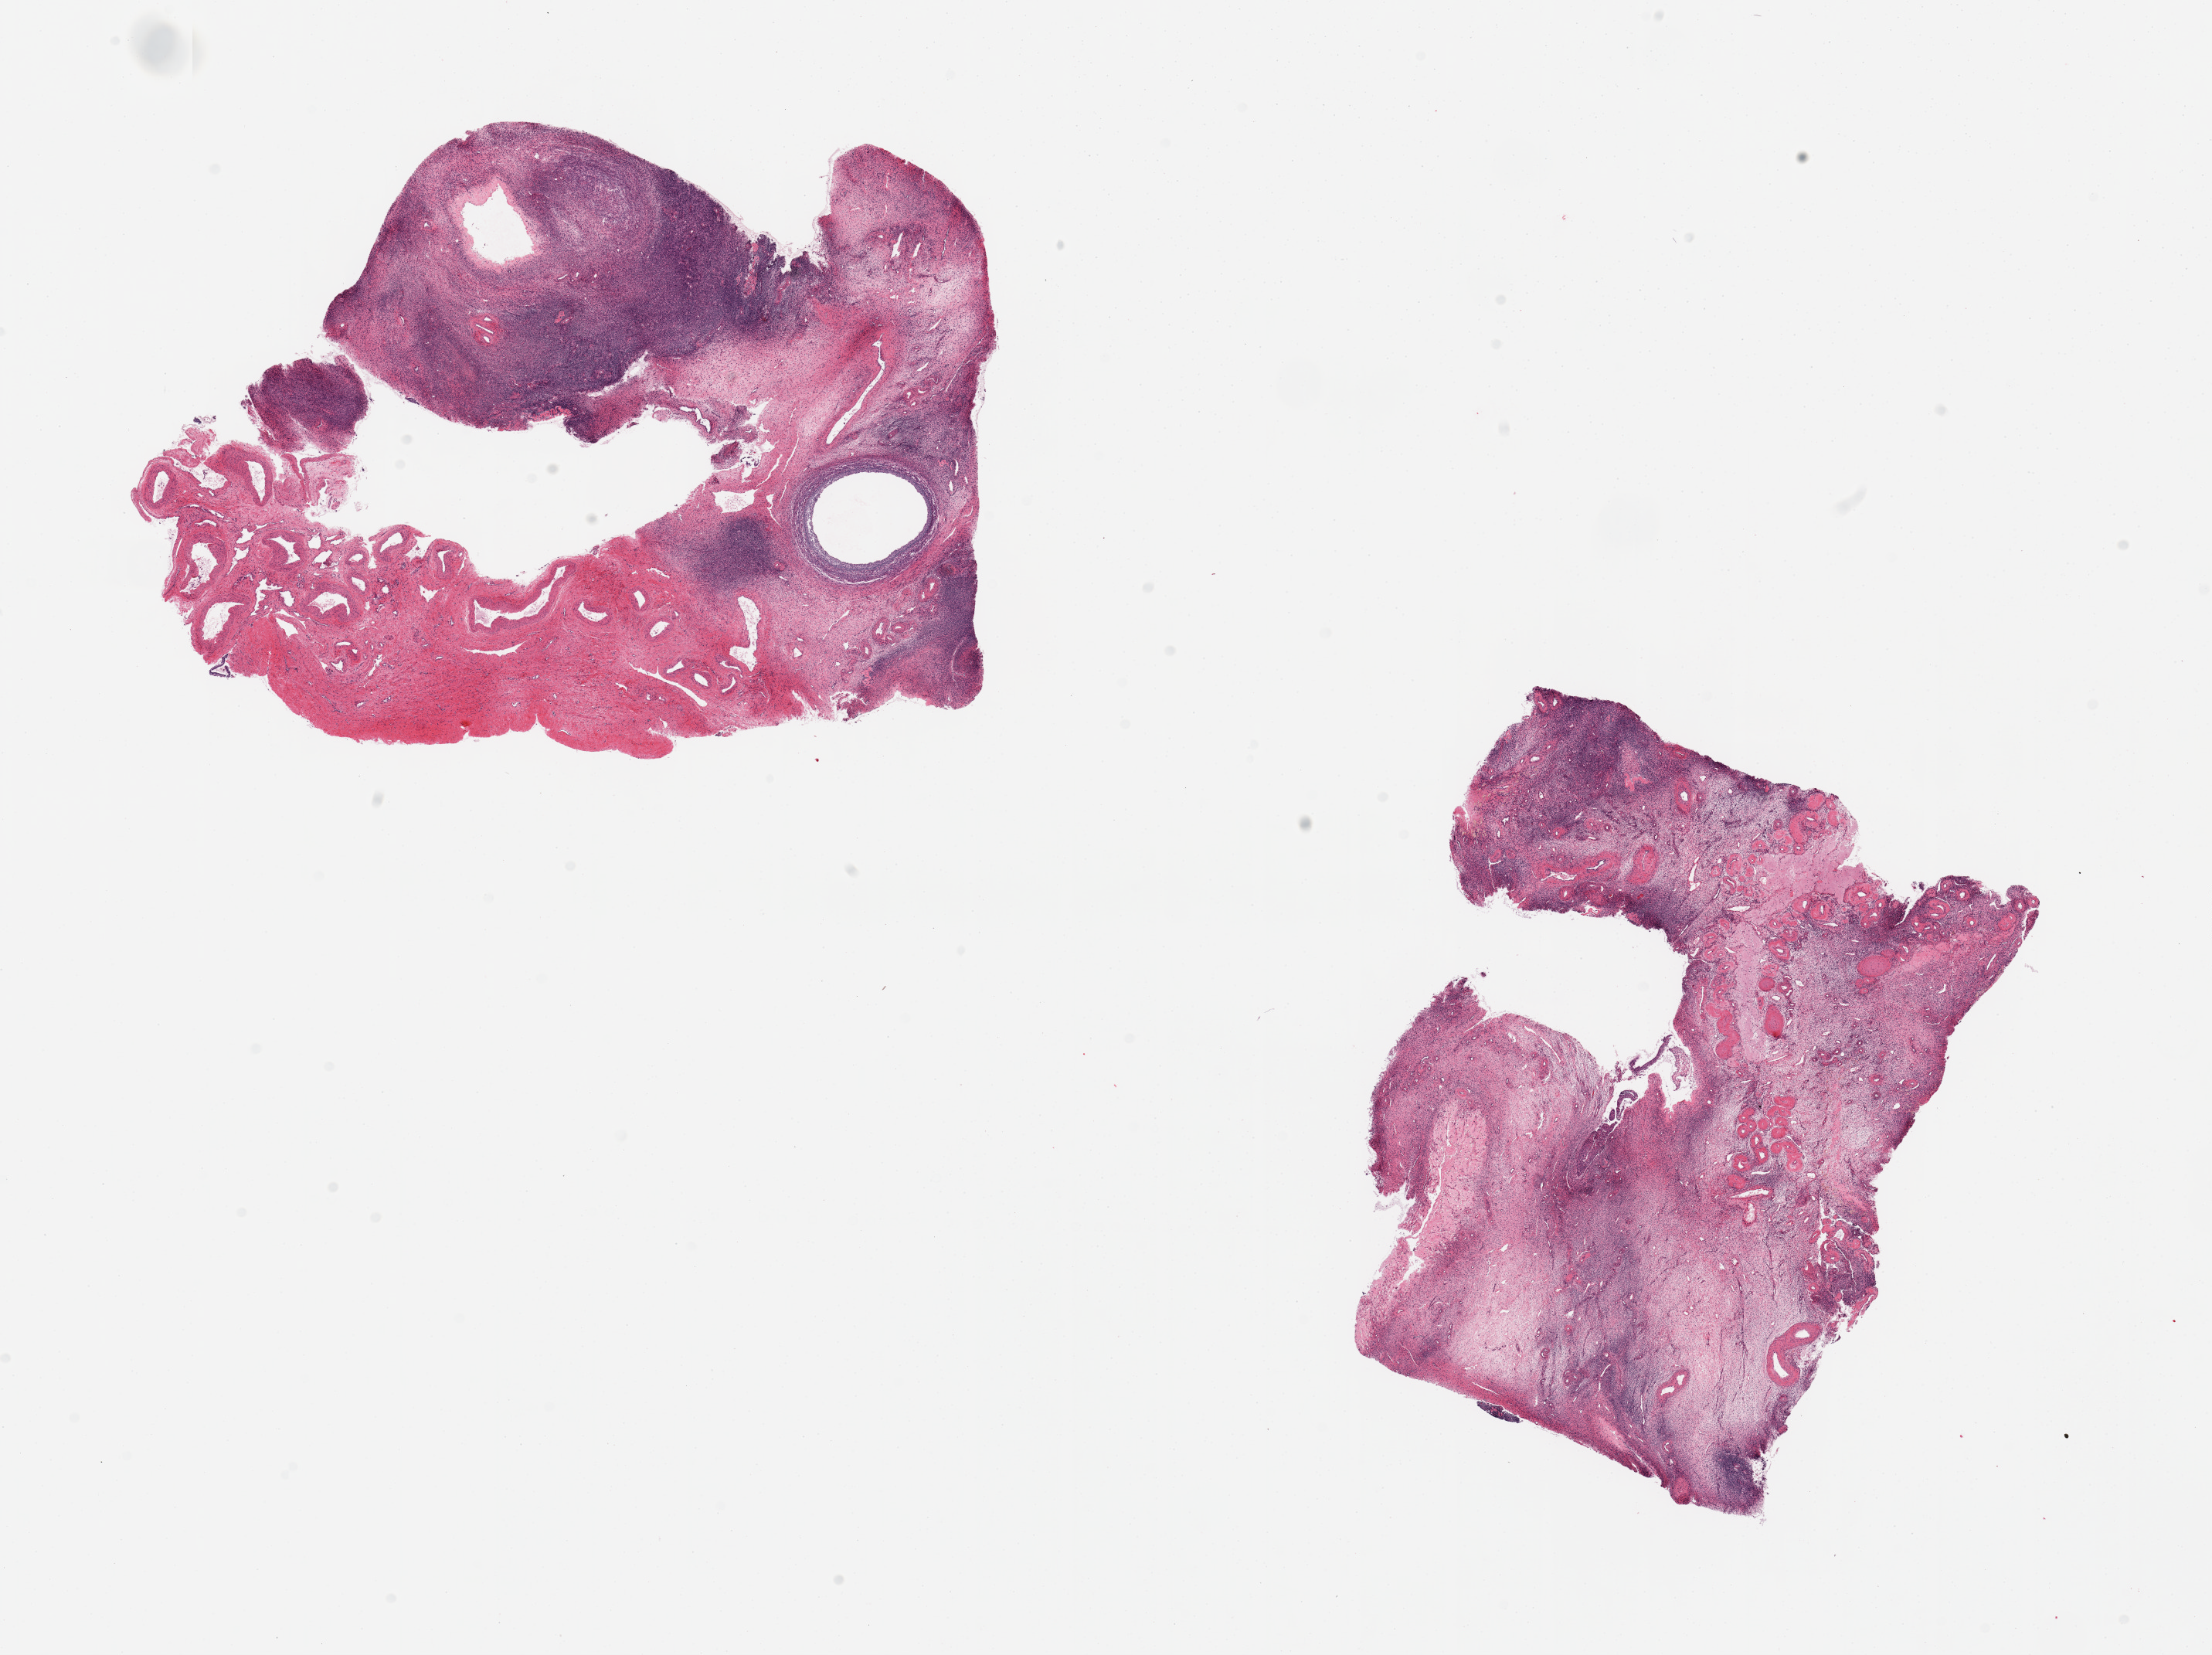
Whole-slide image, H&E stain, brightfield, low-resolution overview of the scanned area, about 22.6 x 16.9 mm (acquisition: 20x scan). PAXgene-fixed paraffin-embedded (PFPE) section. Section of ovary (target tissue). Tissue donor sample. Donor: female.
Reviewer comment on this tissue sample: 2 pieces.